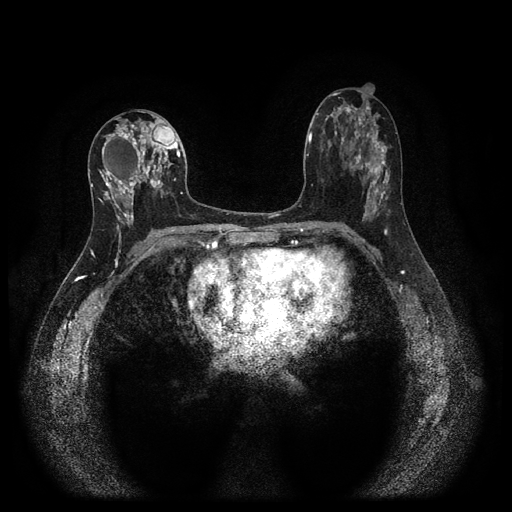
Breast MRI (dynamic contrast-enhanced, multi-phase), one axial slice; slice 53 of 116 in the series (ordered by position); dynamic contrast-enhanced series, time point 2 of 5 at this slice position (early post-contrast); 1.5 T; TE 2.7 ms, TR 5.4 ms; 2 mm slice thickness; 512 × 512 image matrix. Female patient, age 47 years.
Annotated regions visible in this slice (semi-automatic segmentation, software-assisted and operator-edited):
- breast lesion (labelled 'tumour' in the annotation; benign lesions carry a separate 'benign' label): box from (x=94, y=118) to (x=178, y=233) px